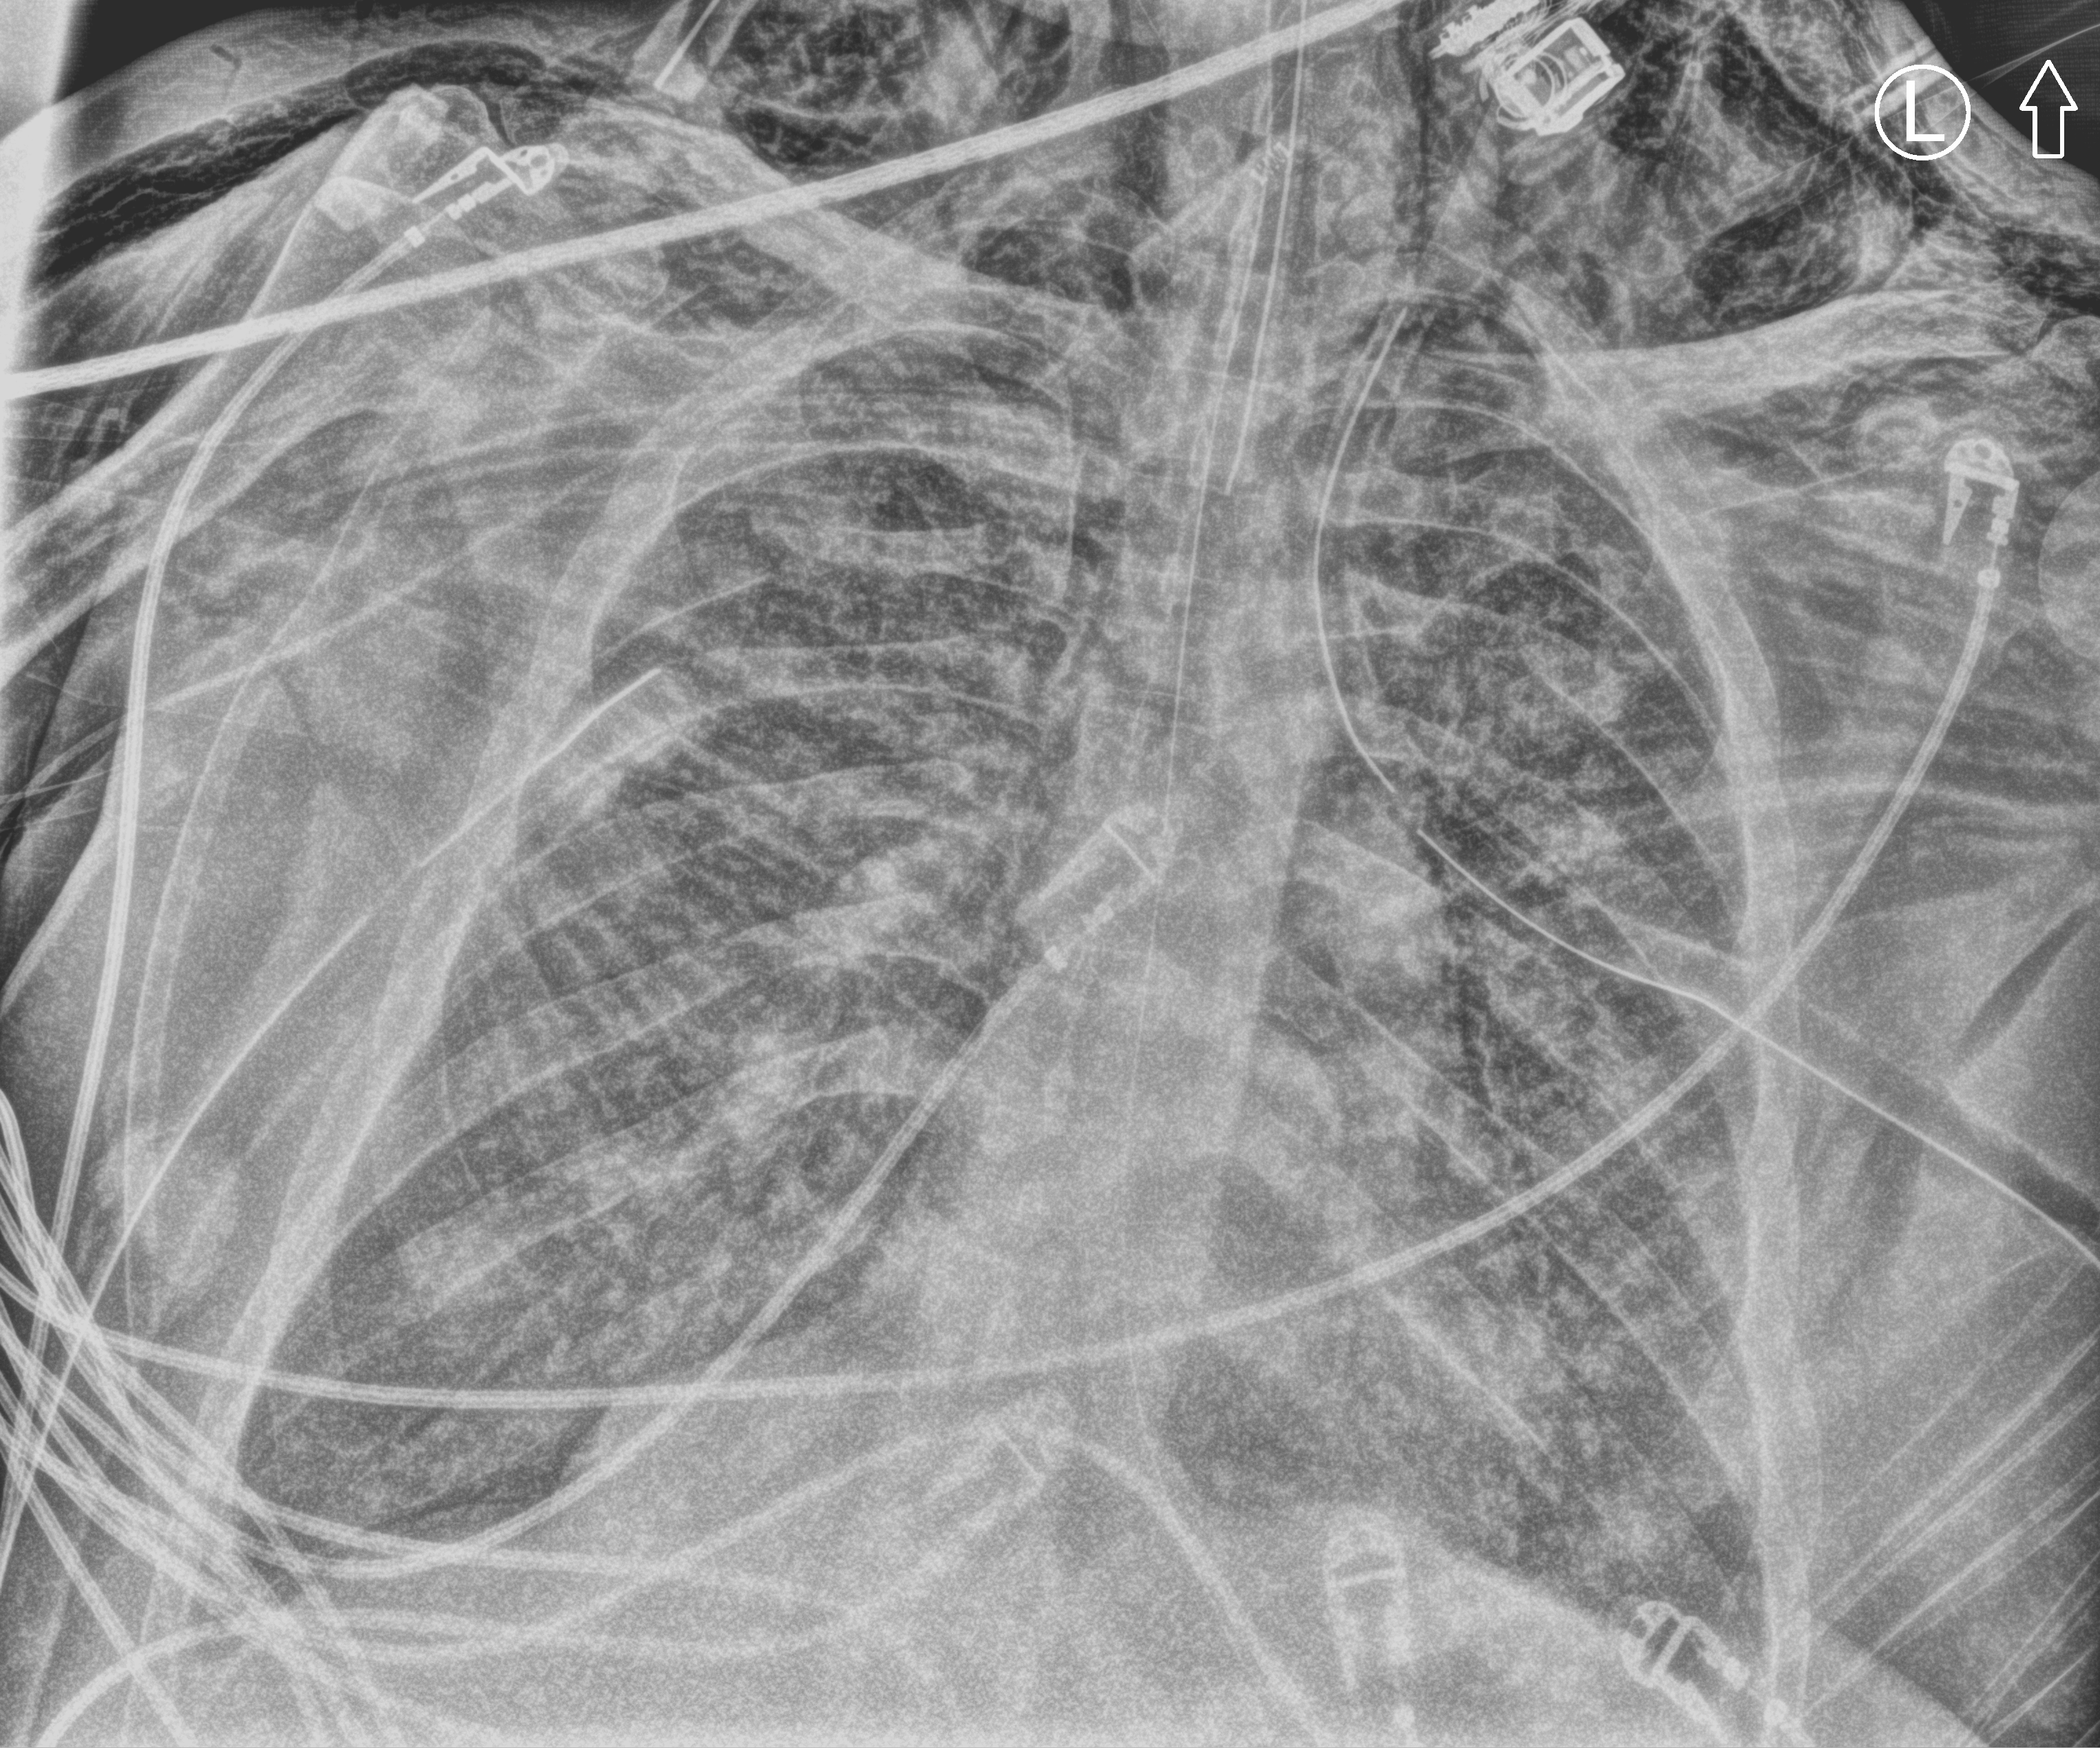
Portable chest radiograph, anteroposterior (AP) projection. Adult patient hospitalised with COVID-19, age 18–59 years.
From the hospital-stay record, not from the radiograph (when in the stay this image was taken is not recorded): COPD (admission record): no; admitted to intensive care during this hospital stay: yes.